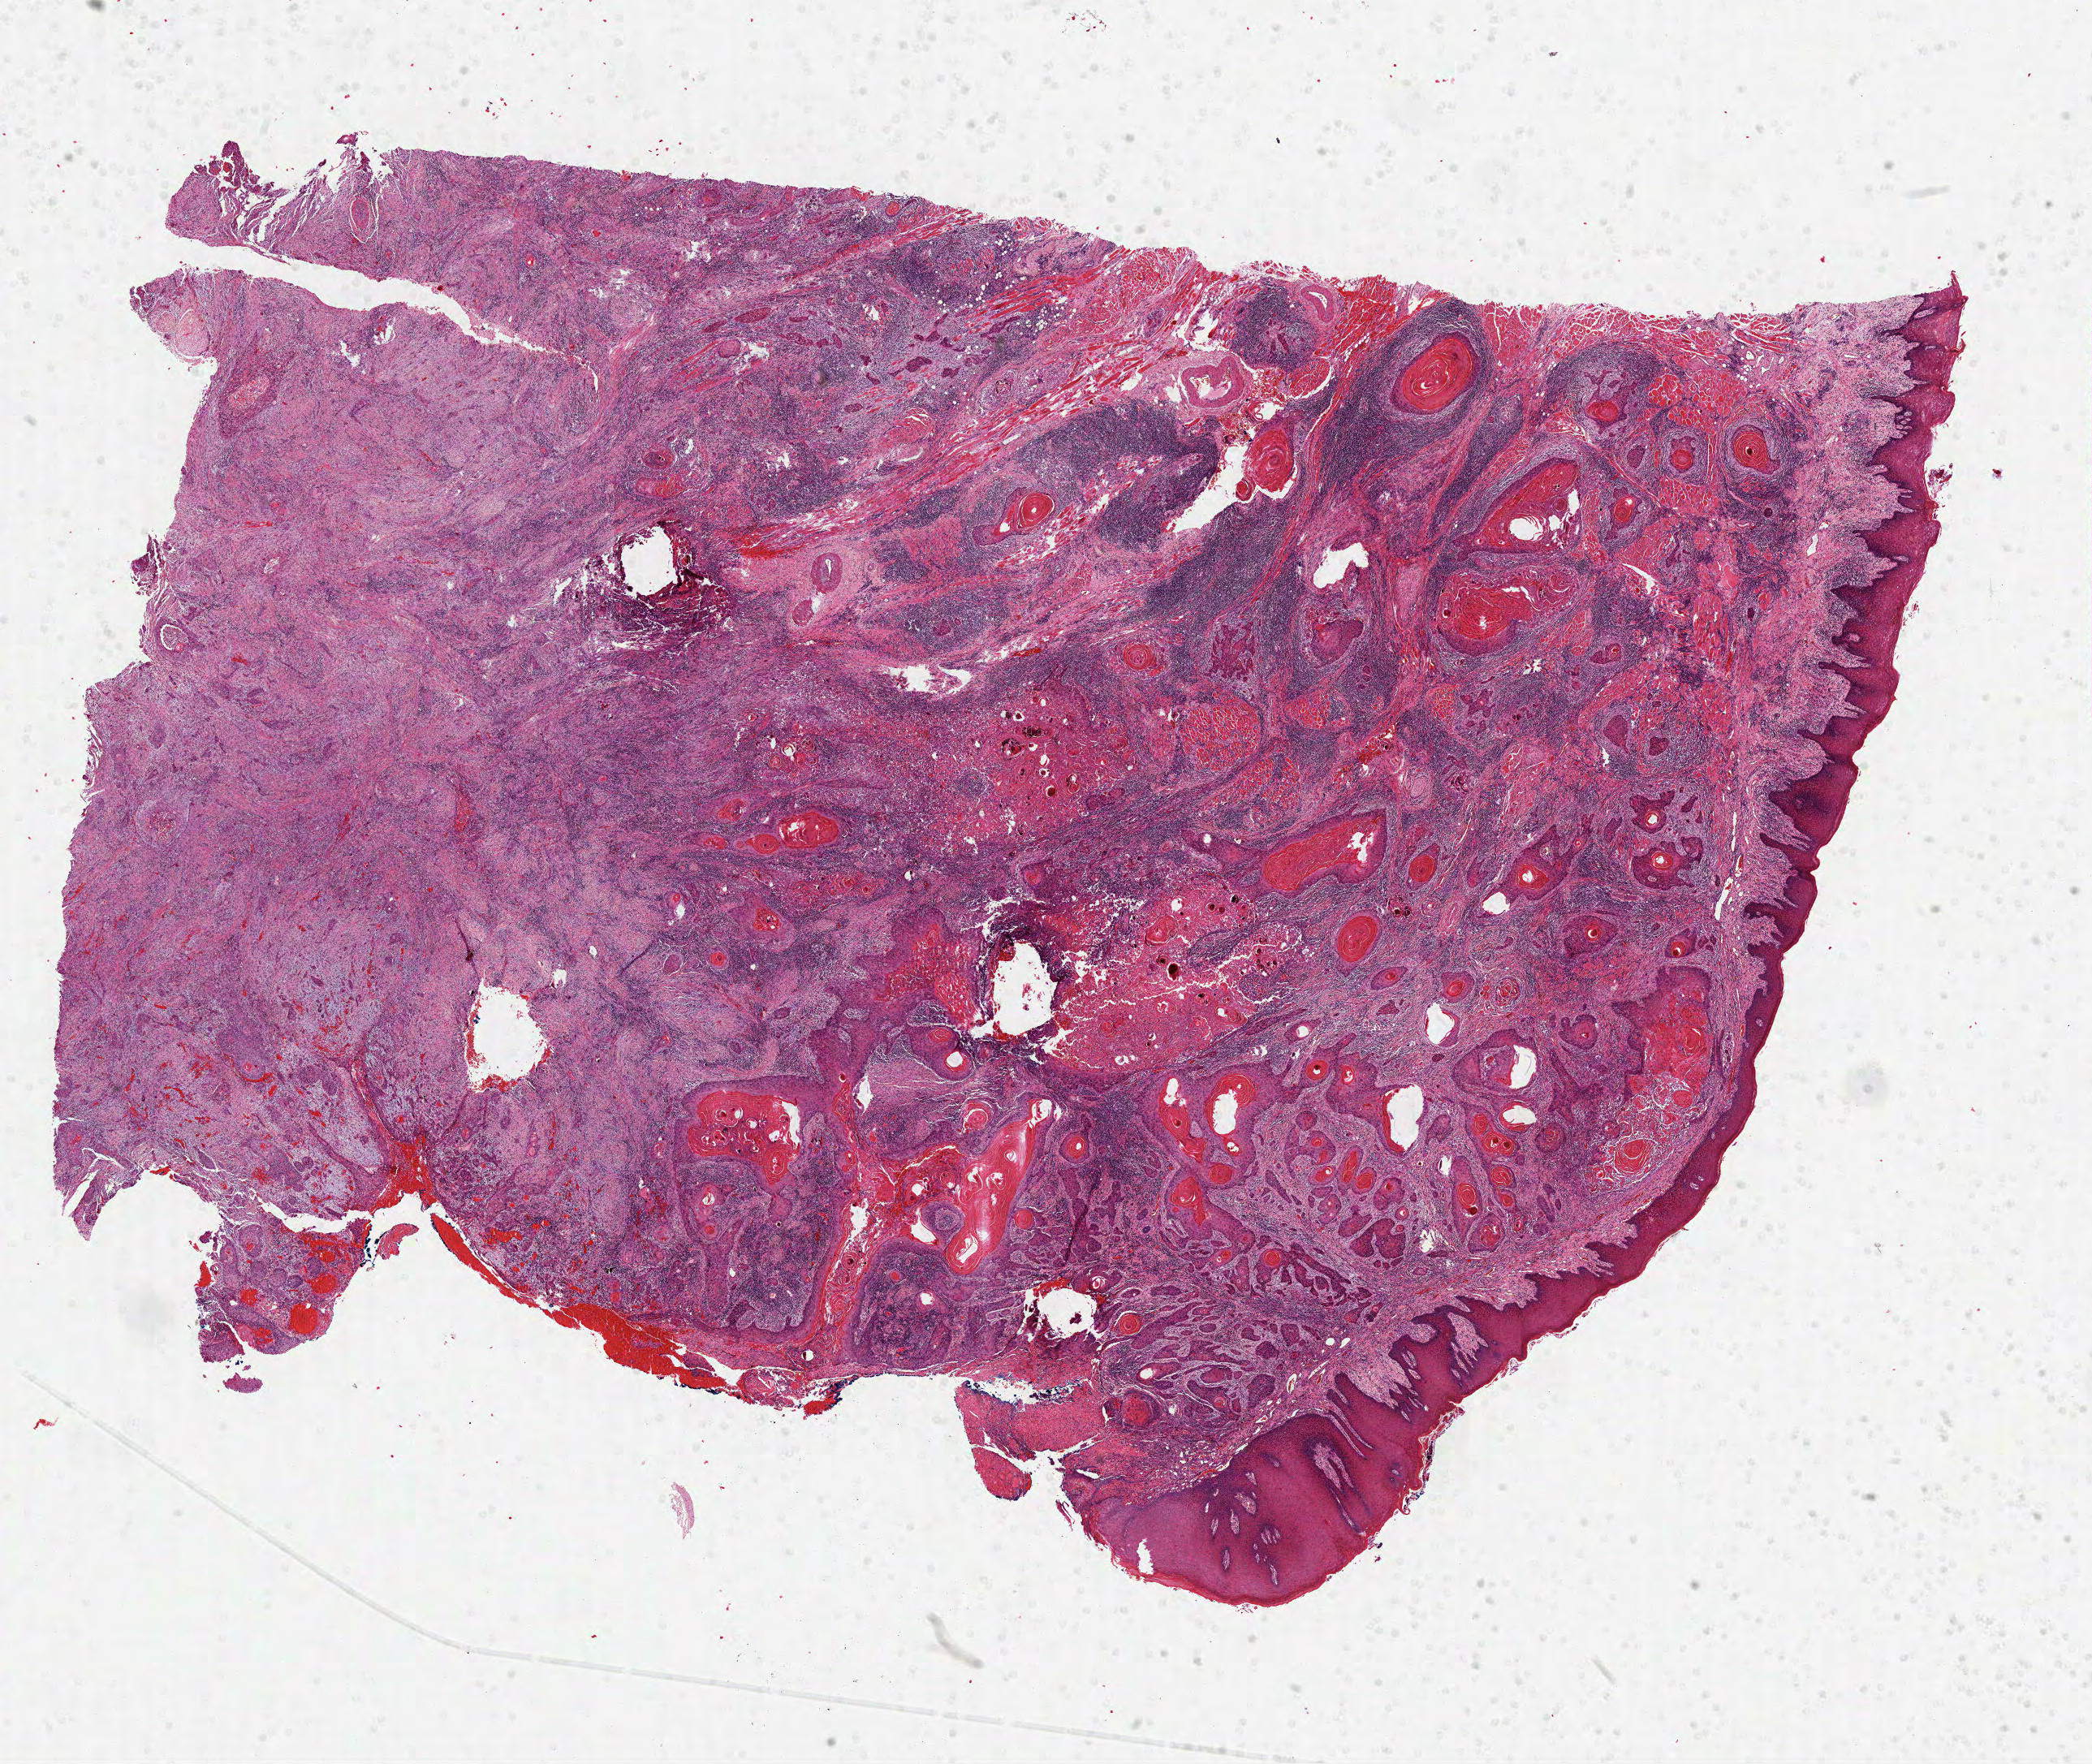
Hematoxylin and eosin (H&E) stained whole-slide image — whole scanned area (about 20.8 x 17.5 mm) shown as a low-resolution overview. Formalin-fixed paraffin-embedded (FFPE) diagnostic section. Sample: primary tumour, head and neck. Patient: male, age at initial diagnosis 74 years. Histologic grade: G2 (moderately differentiated).
- histologic diagnosis: Squamous cell carcinoma, NOS (tongue, NOS)
- laterality: right
- TNM: T2 N2
- AJCC pathologic stage: IVA